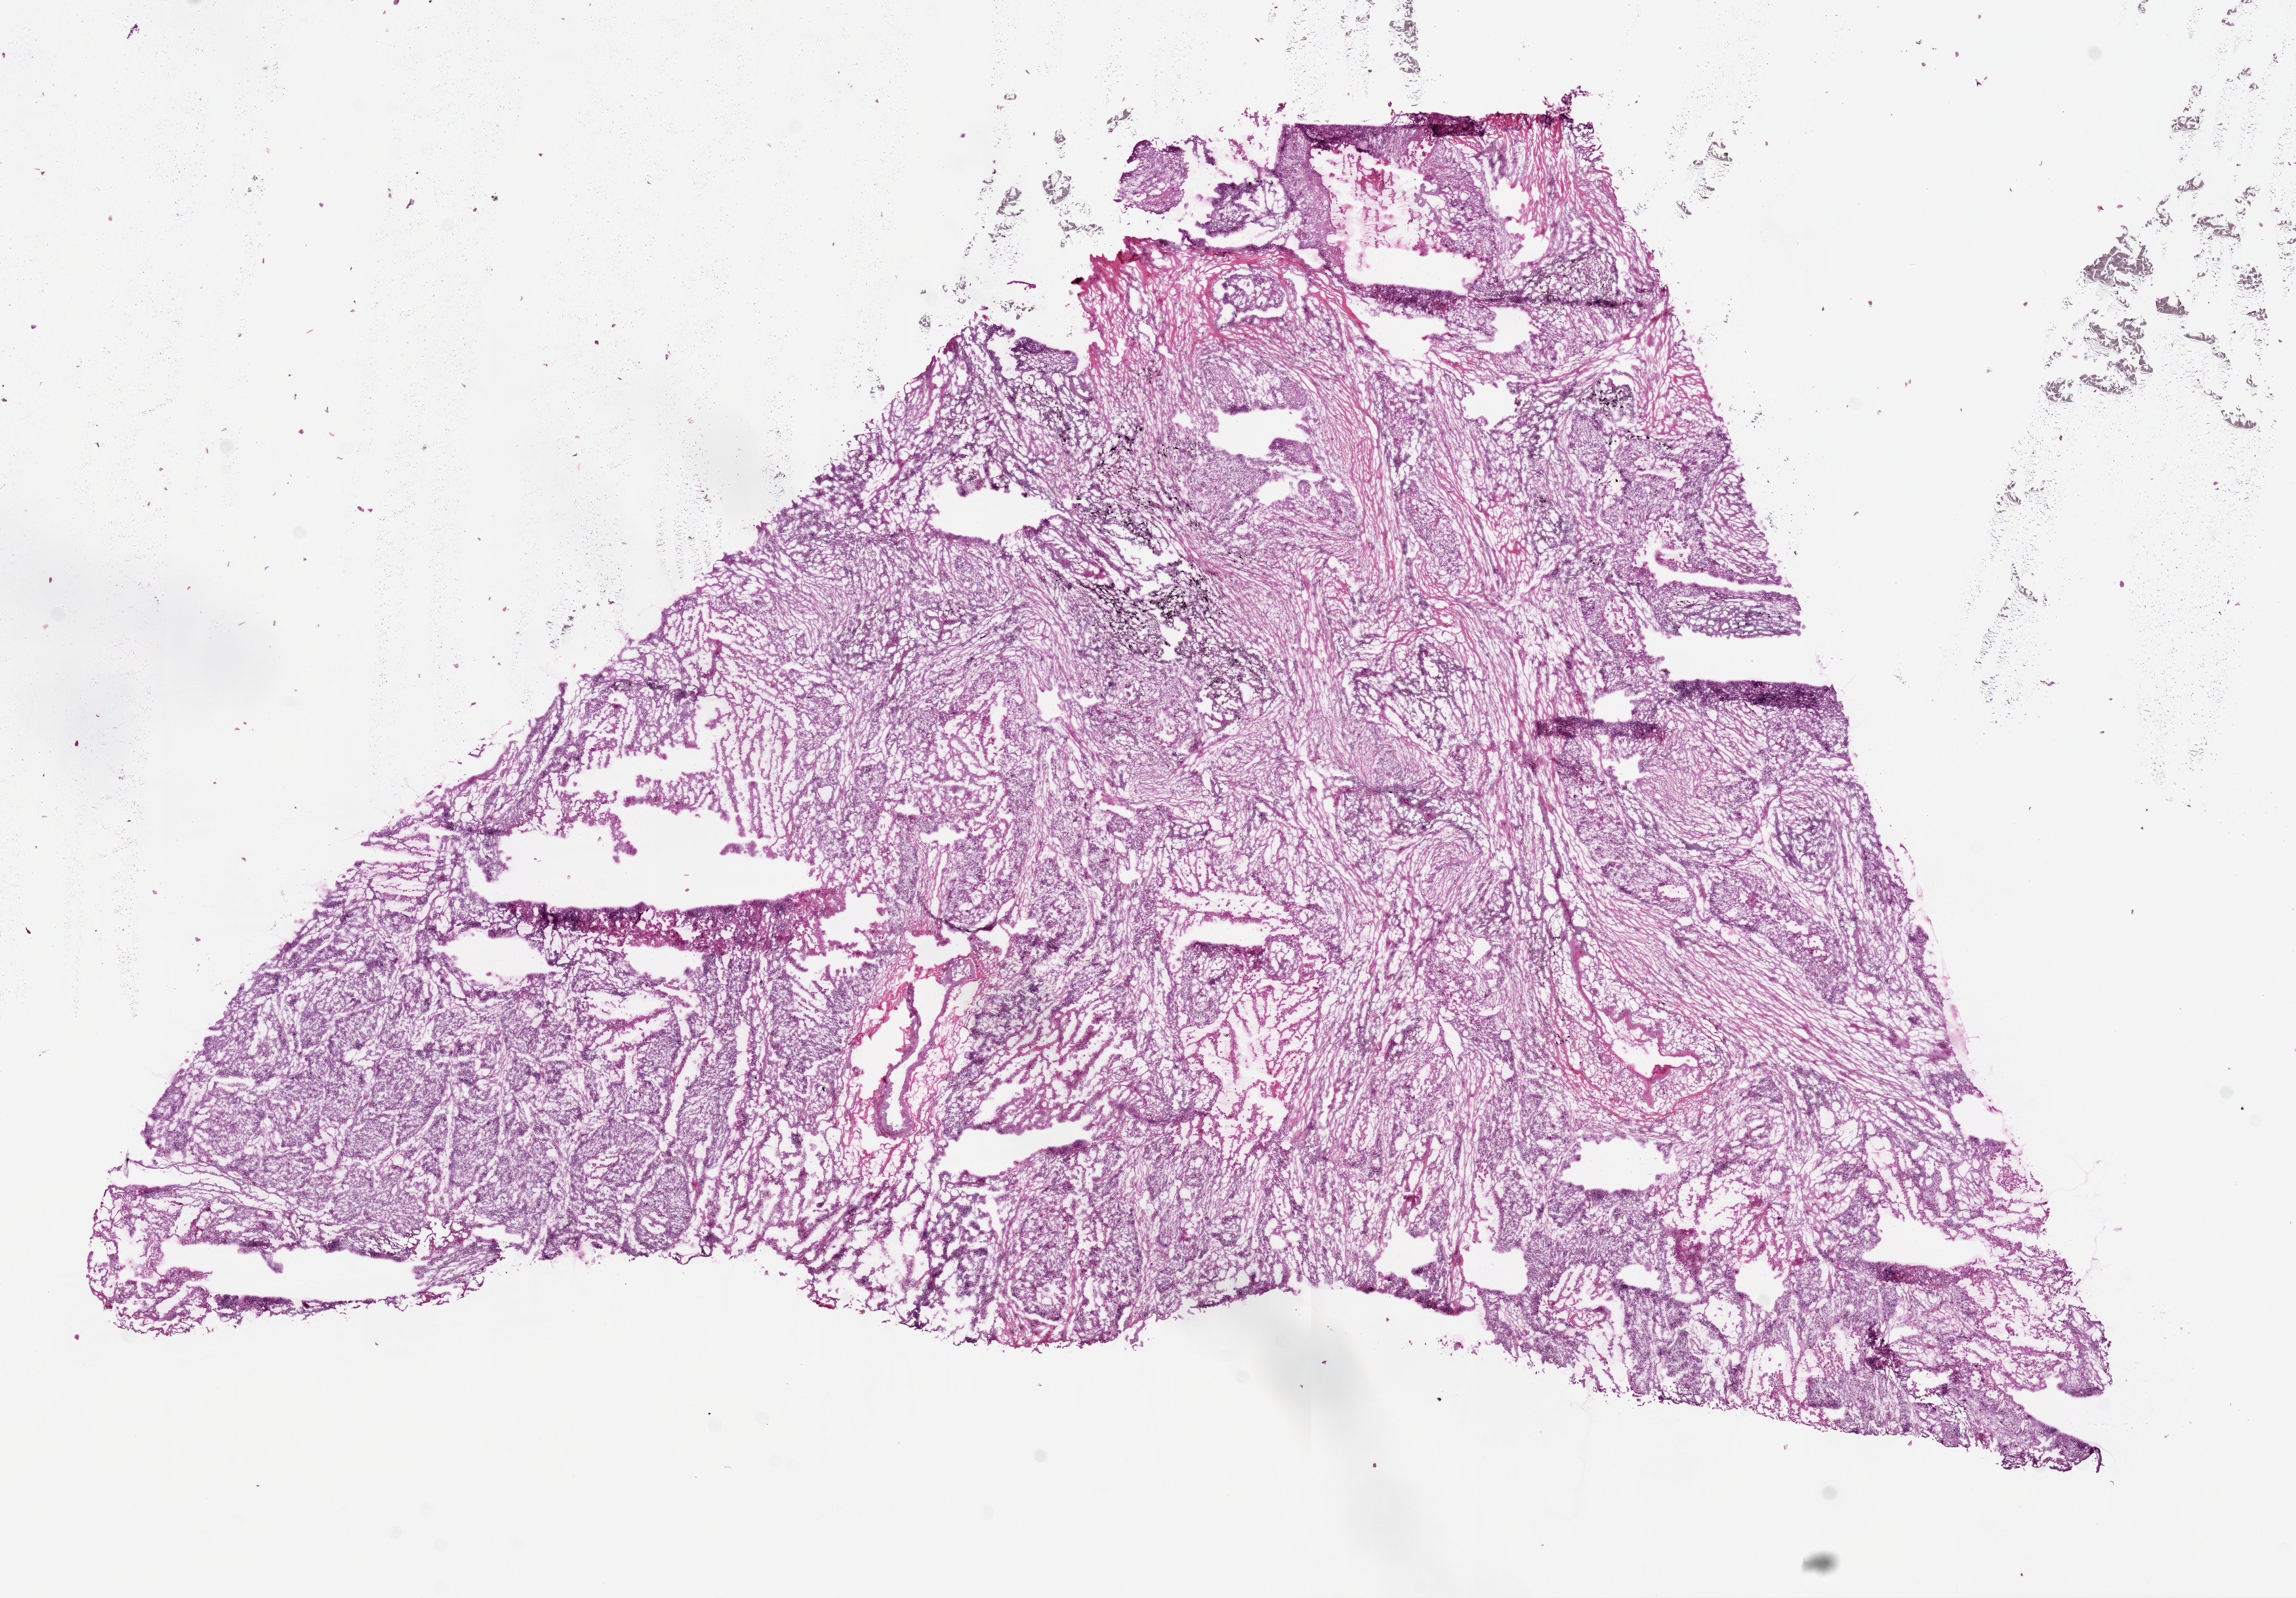
Digitized H&E-stained tissue section (whole slide) — low-resolution overview of the scanned area, about 14.0 x 9.8 mm; frozen section from the top of the tissue portion; lung, primary tumour sample. Female, age 68 years at initial diagnosis. Pathologist review of this section (percent, as recorded): tumour cells 90%, tumour nuclei 72%, normal cells 0%, stromal cells 0%, necrosis 10%. Infiltration values recorded for this section: lymphocyte infiltration 10%, monocyte infiltration 5%, neutrophil infiltration 0%.
Laterality: left. AJCC pathologic stage: IB. TNM: T2 N0 M0. Pathologic diagnosis: Squamous cell carcinoma, NOS.